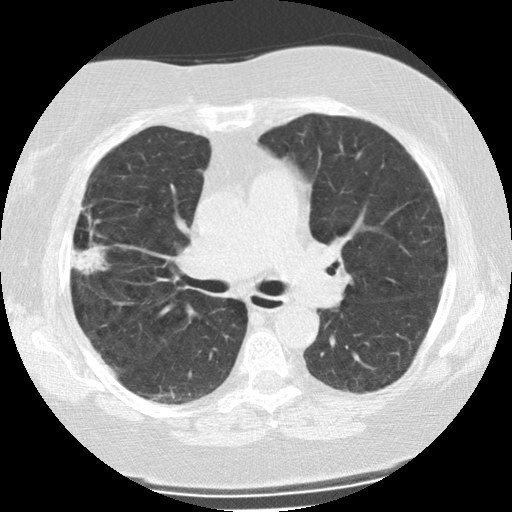
Low-dose screening chest CT, one axial slice; position 139 of 225 along the scan axis; reconstruction kernel STANDARD; 120 kVp; lung window (W 1500 / L -600 HU); 2.5 mm slice thickness; 512 × 512 image matrix, field of view 320 × 320 mm.
Annotated regions visible in this slice (manually delineated by an expert):
- lesion 1 (tumor, upper lobe of right lung): bounding box <72,244,108,275> (left, top, right, bottom; pixels)